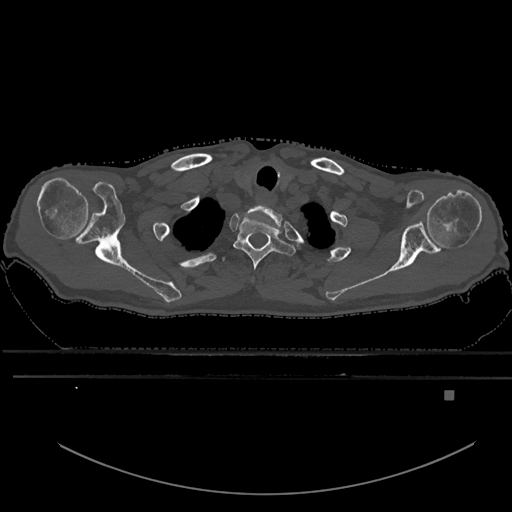
CT including the spine, one axial slice; slice 538 of 969 in the series (ordered by position); bone window (W 1800 / L 400 HU); 0.5 mm slice thickness; 512 × 512 image matrix, field of view 456 × 456 mm. Male patient, age 82 years. From the clinical record (not read from this slice): primary cancer: prostate; vertebrae with lytic lesions (as recorded): T11, T9, T8, T2.
Structures marked on this image (semi-automatically segmented with operator editing):
- T1 vertebra: bounding box <233,217,295,271> (left, top, right, bottom; pixels)
- T2 vertebra: <221,256,227,263>